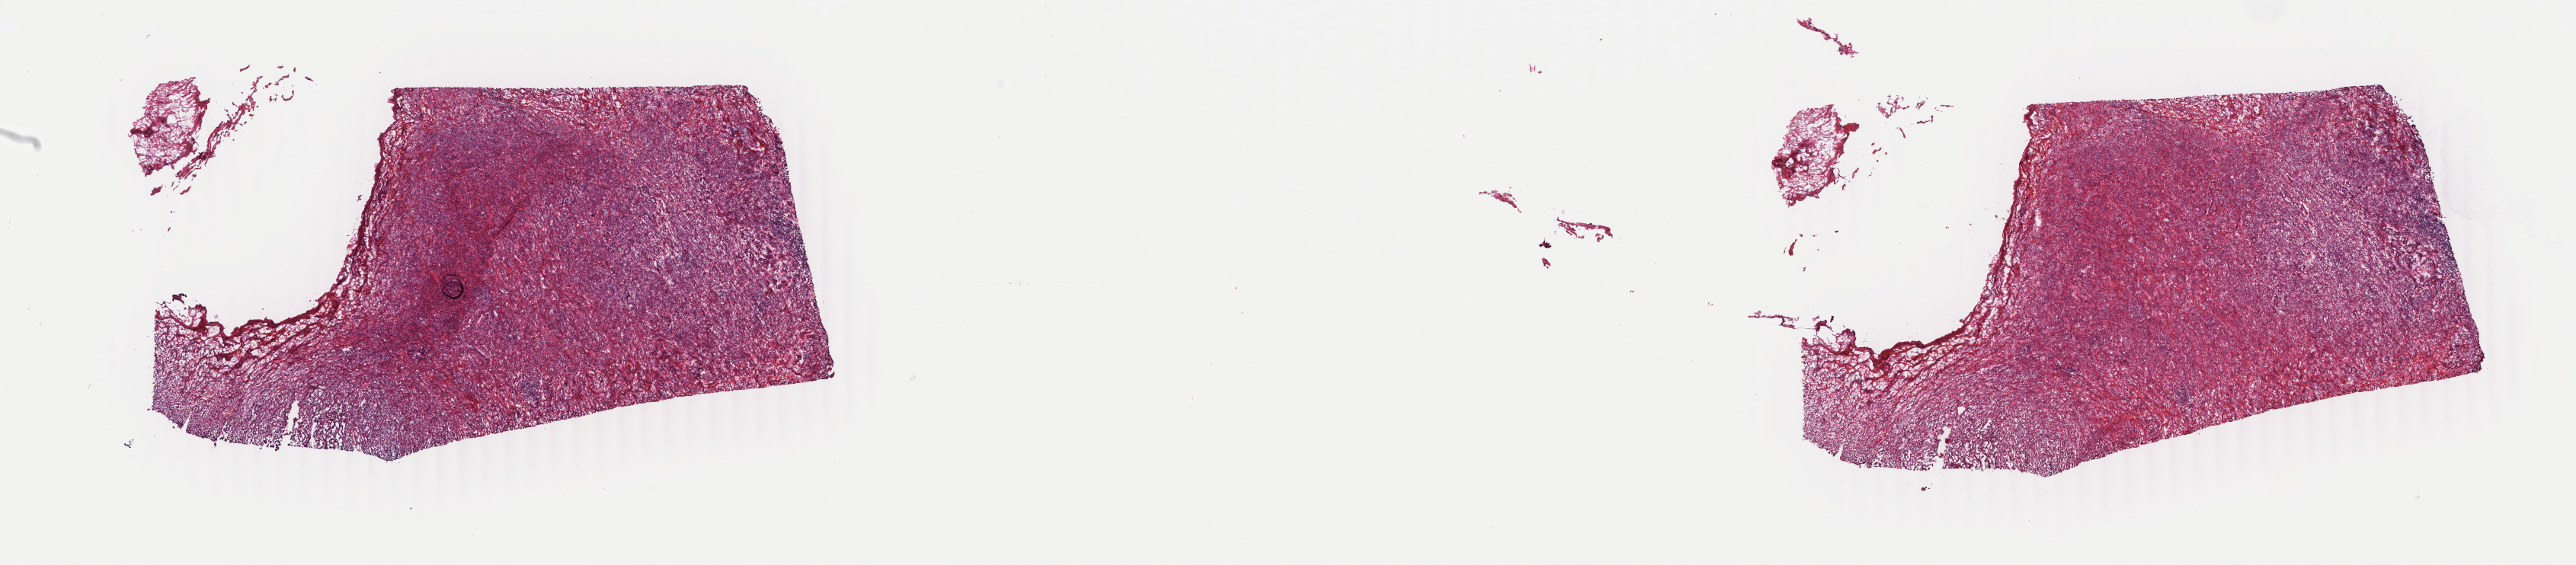
Whole-slide histology image, H&E, a low-resolution overview of the entire scanned area, about 26.9 x 5.9 mm (from a 40x scan). Frozen section. Mesothelium, primary tumour sample. Male patient; age at initial diagnosis 80 years. Pathologist review of this section (percent, as recorded): tumour cells 40%, tumour nuclei 95%, normal cells 0%, stromal cells 60%, necrosis 0%. Infiltration values recorded for this section: lymphocyte infiltration 4%, monocyte infiltration 1%, neutrophil infiltration 0%.
Diagnosis: Mesothelioma, biphasic, malignant (pleura, NOS). AJCC pathologic stage: III (7th edition).